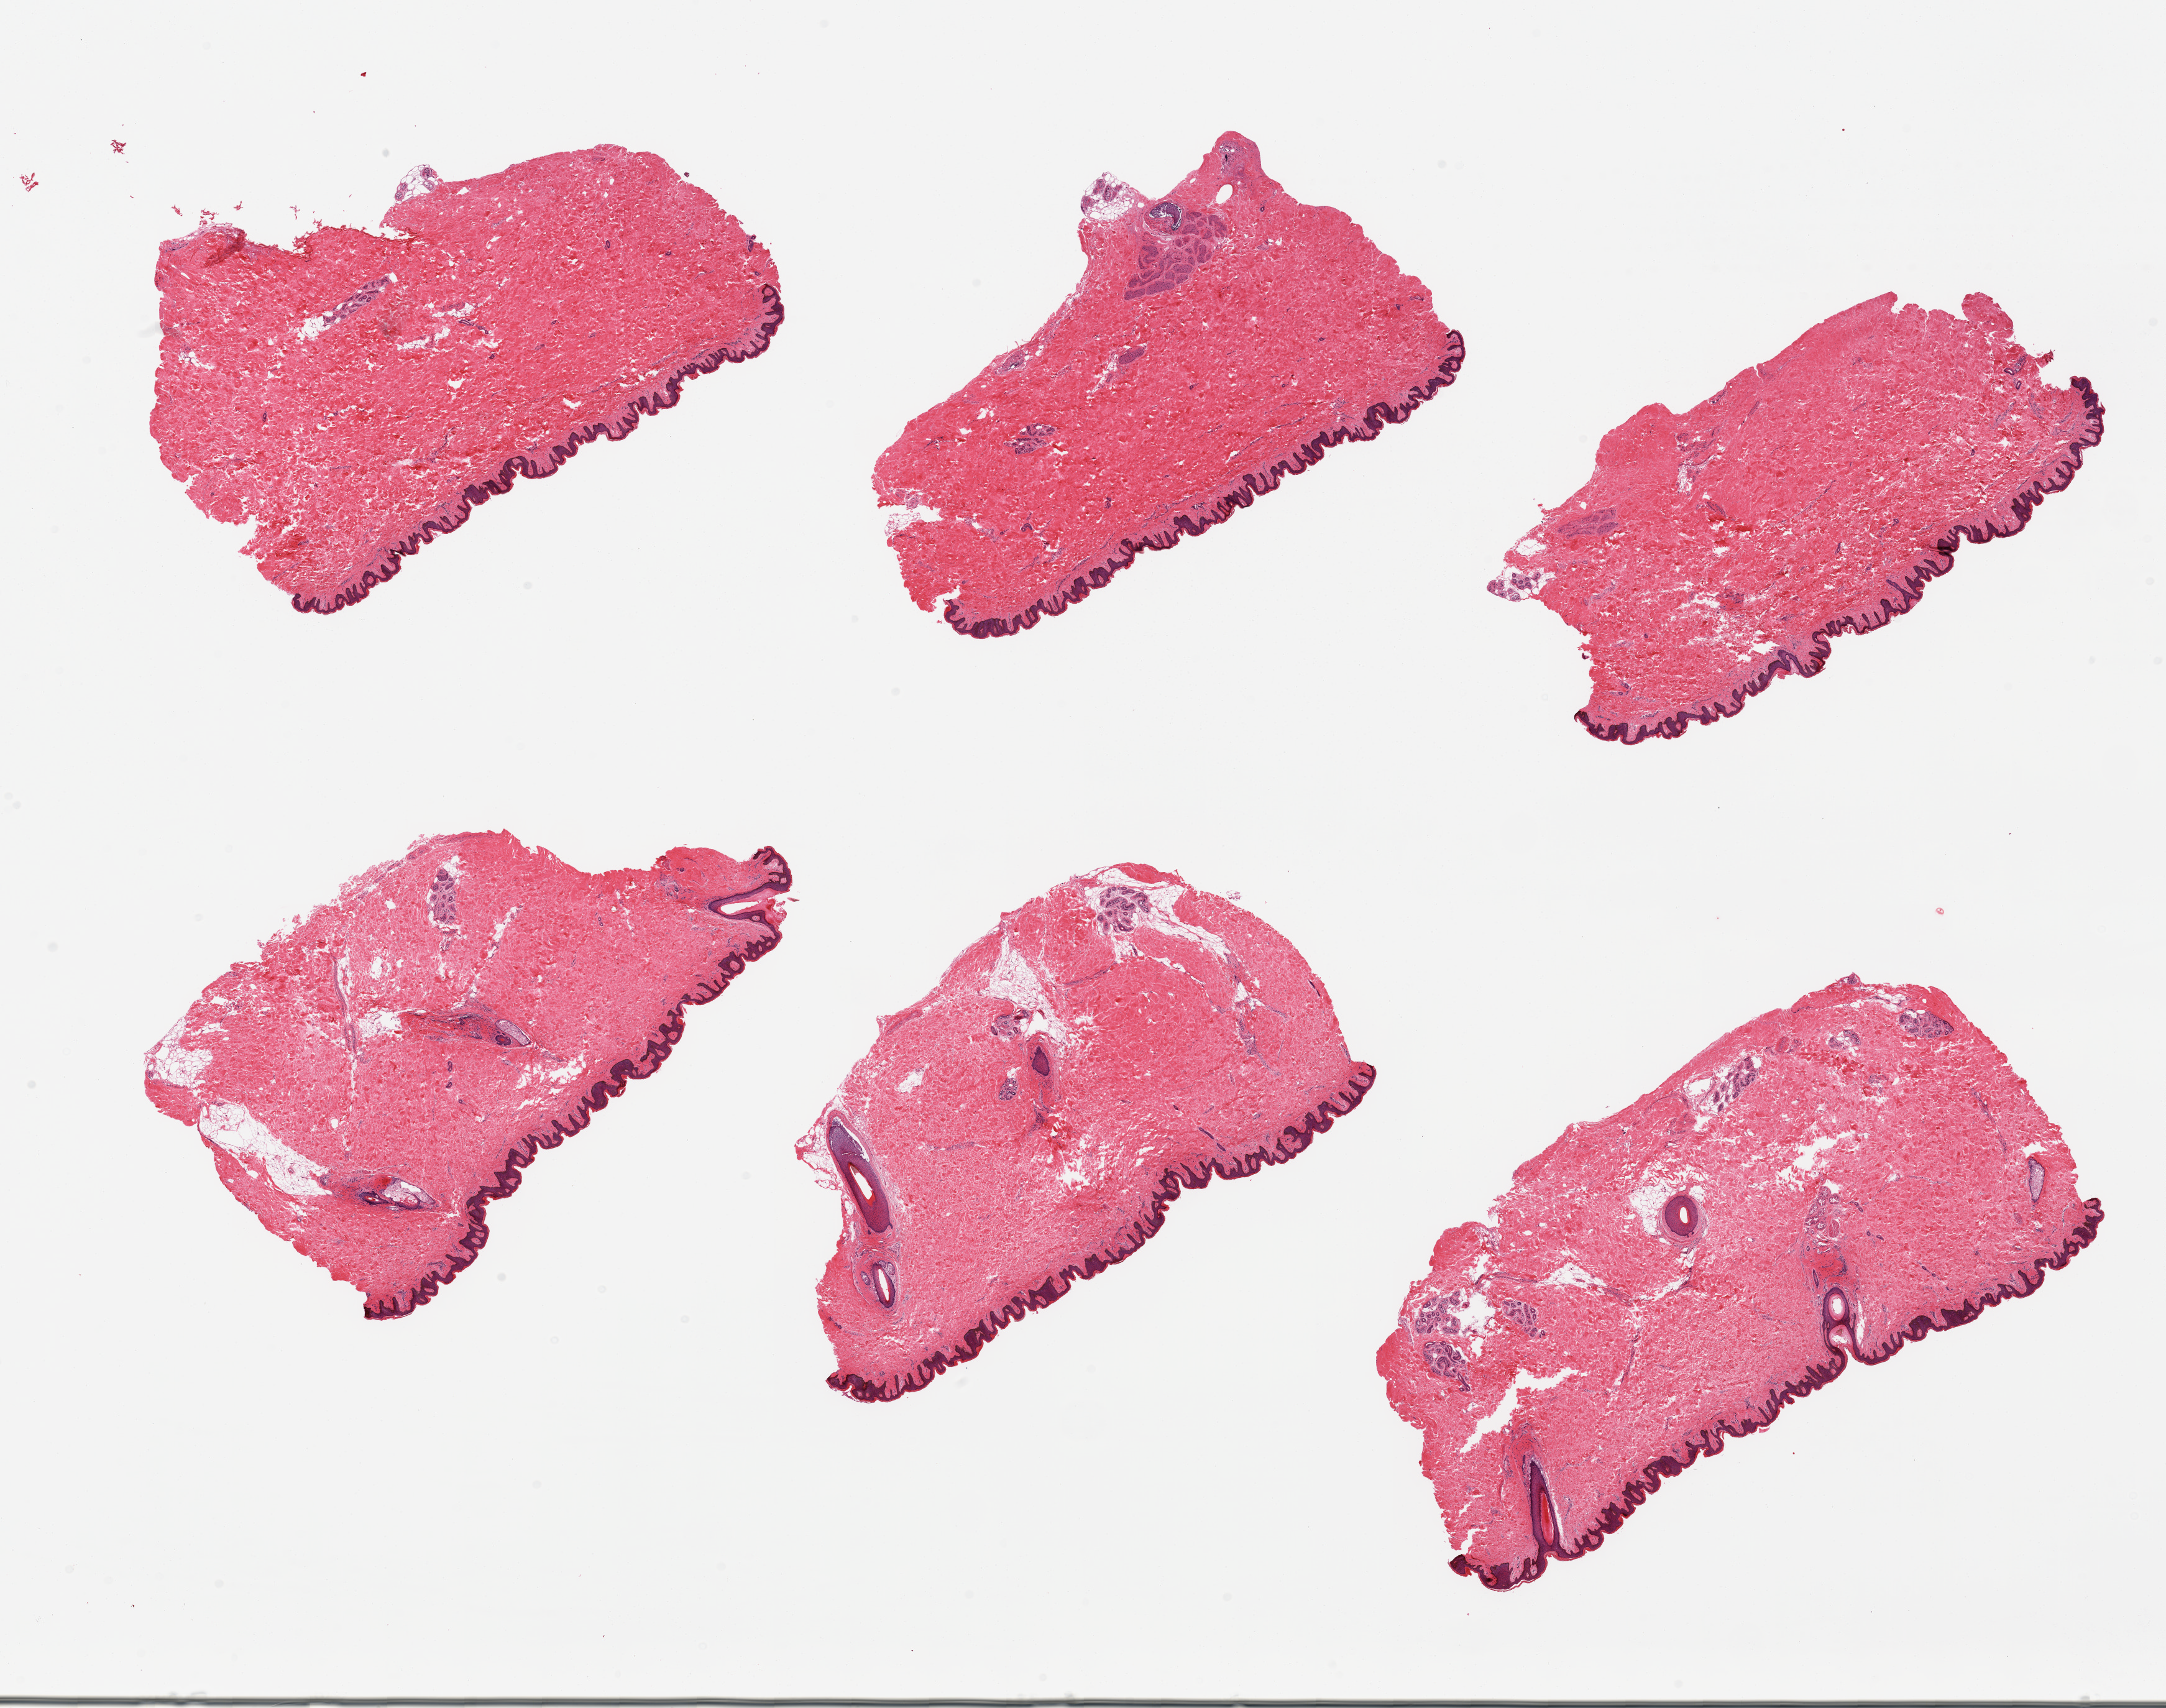
Digitized H&E-stained section, whole scanned area (about 27.6 x 21.7 mm) shown as a low-resolution overview, PAXgene-fixed paraffin-embedded (PFPE) section, section of skin of suprapubic region (target tissue), tissue donor sample. Donor sex: male.
Pathologist's review note for this sample: 6 pieces; well trimmed; 3 pieces have 10% intradermal fat, 3 have no measurable fat.